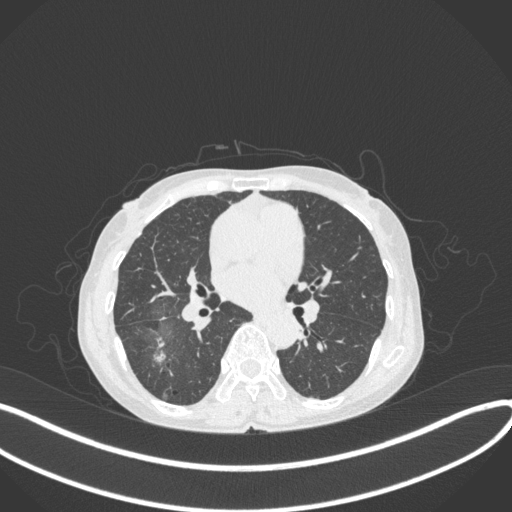
Chest CT, one axial slice; position 202 of 379 along the scan axis; 120 kVp; lung window (W 1500 / L -600 HU); 1 mm slice thickness; 512 × 512 image matrix. Female patient, age 69 years. From the clinical record (not read from this slice): clinical TNM (as recorded): T1b N0 M0; histopathological grade: G2-3.
Structures marked on this image (bounding box drawn by a radiologist):
- lung tumour (recorded histology: adenocarcinoma): box from (x=147, y=333) to (x=174, y=371) px